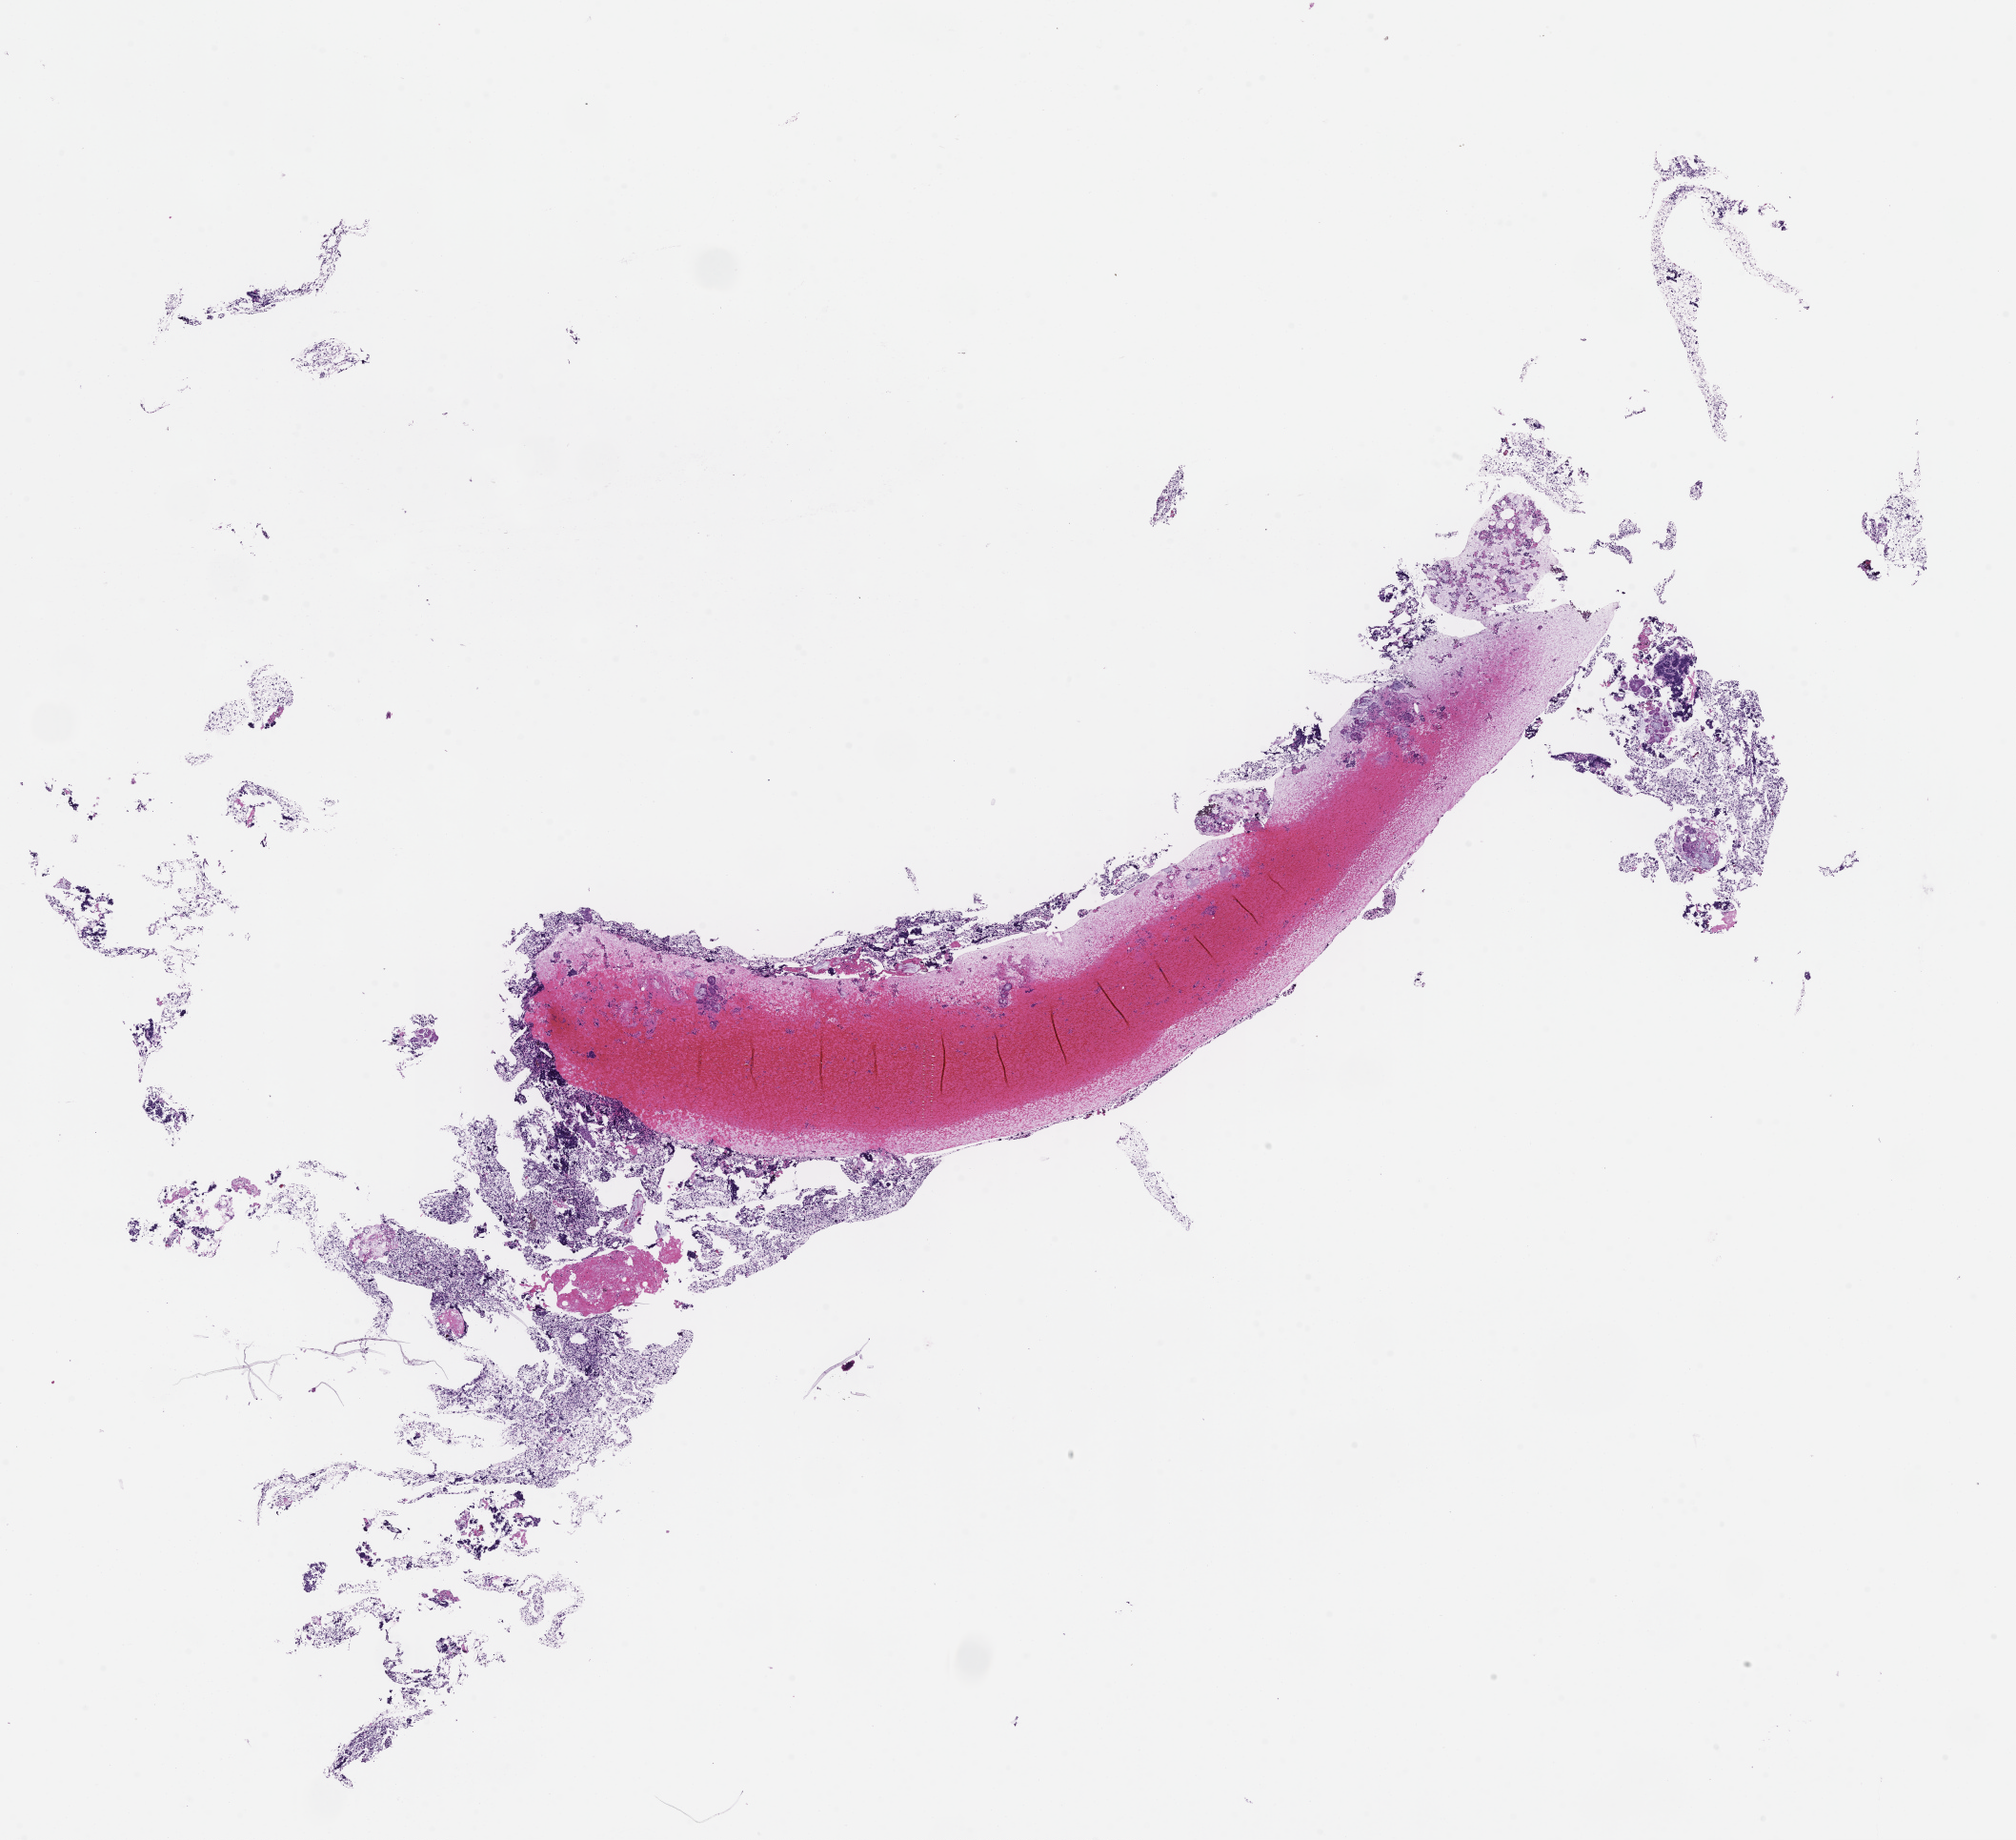
Whole-slide image, hematoxylin and eosin (H&E) stain — shown as a low-resolution overview of the whole scanned area (about 17.1 x 15.6 mm), FFPE section, tissue site: bone marrow, specimen time point: archival tissue. Patient: male.
This section: primary tumor. Diagnosis: Plasma Cell Myeloma.